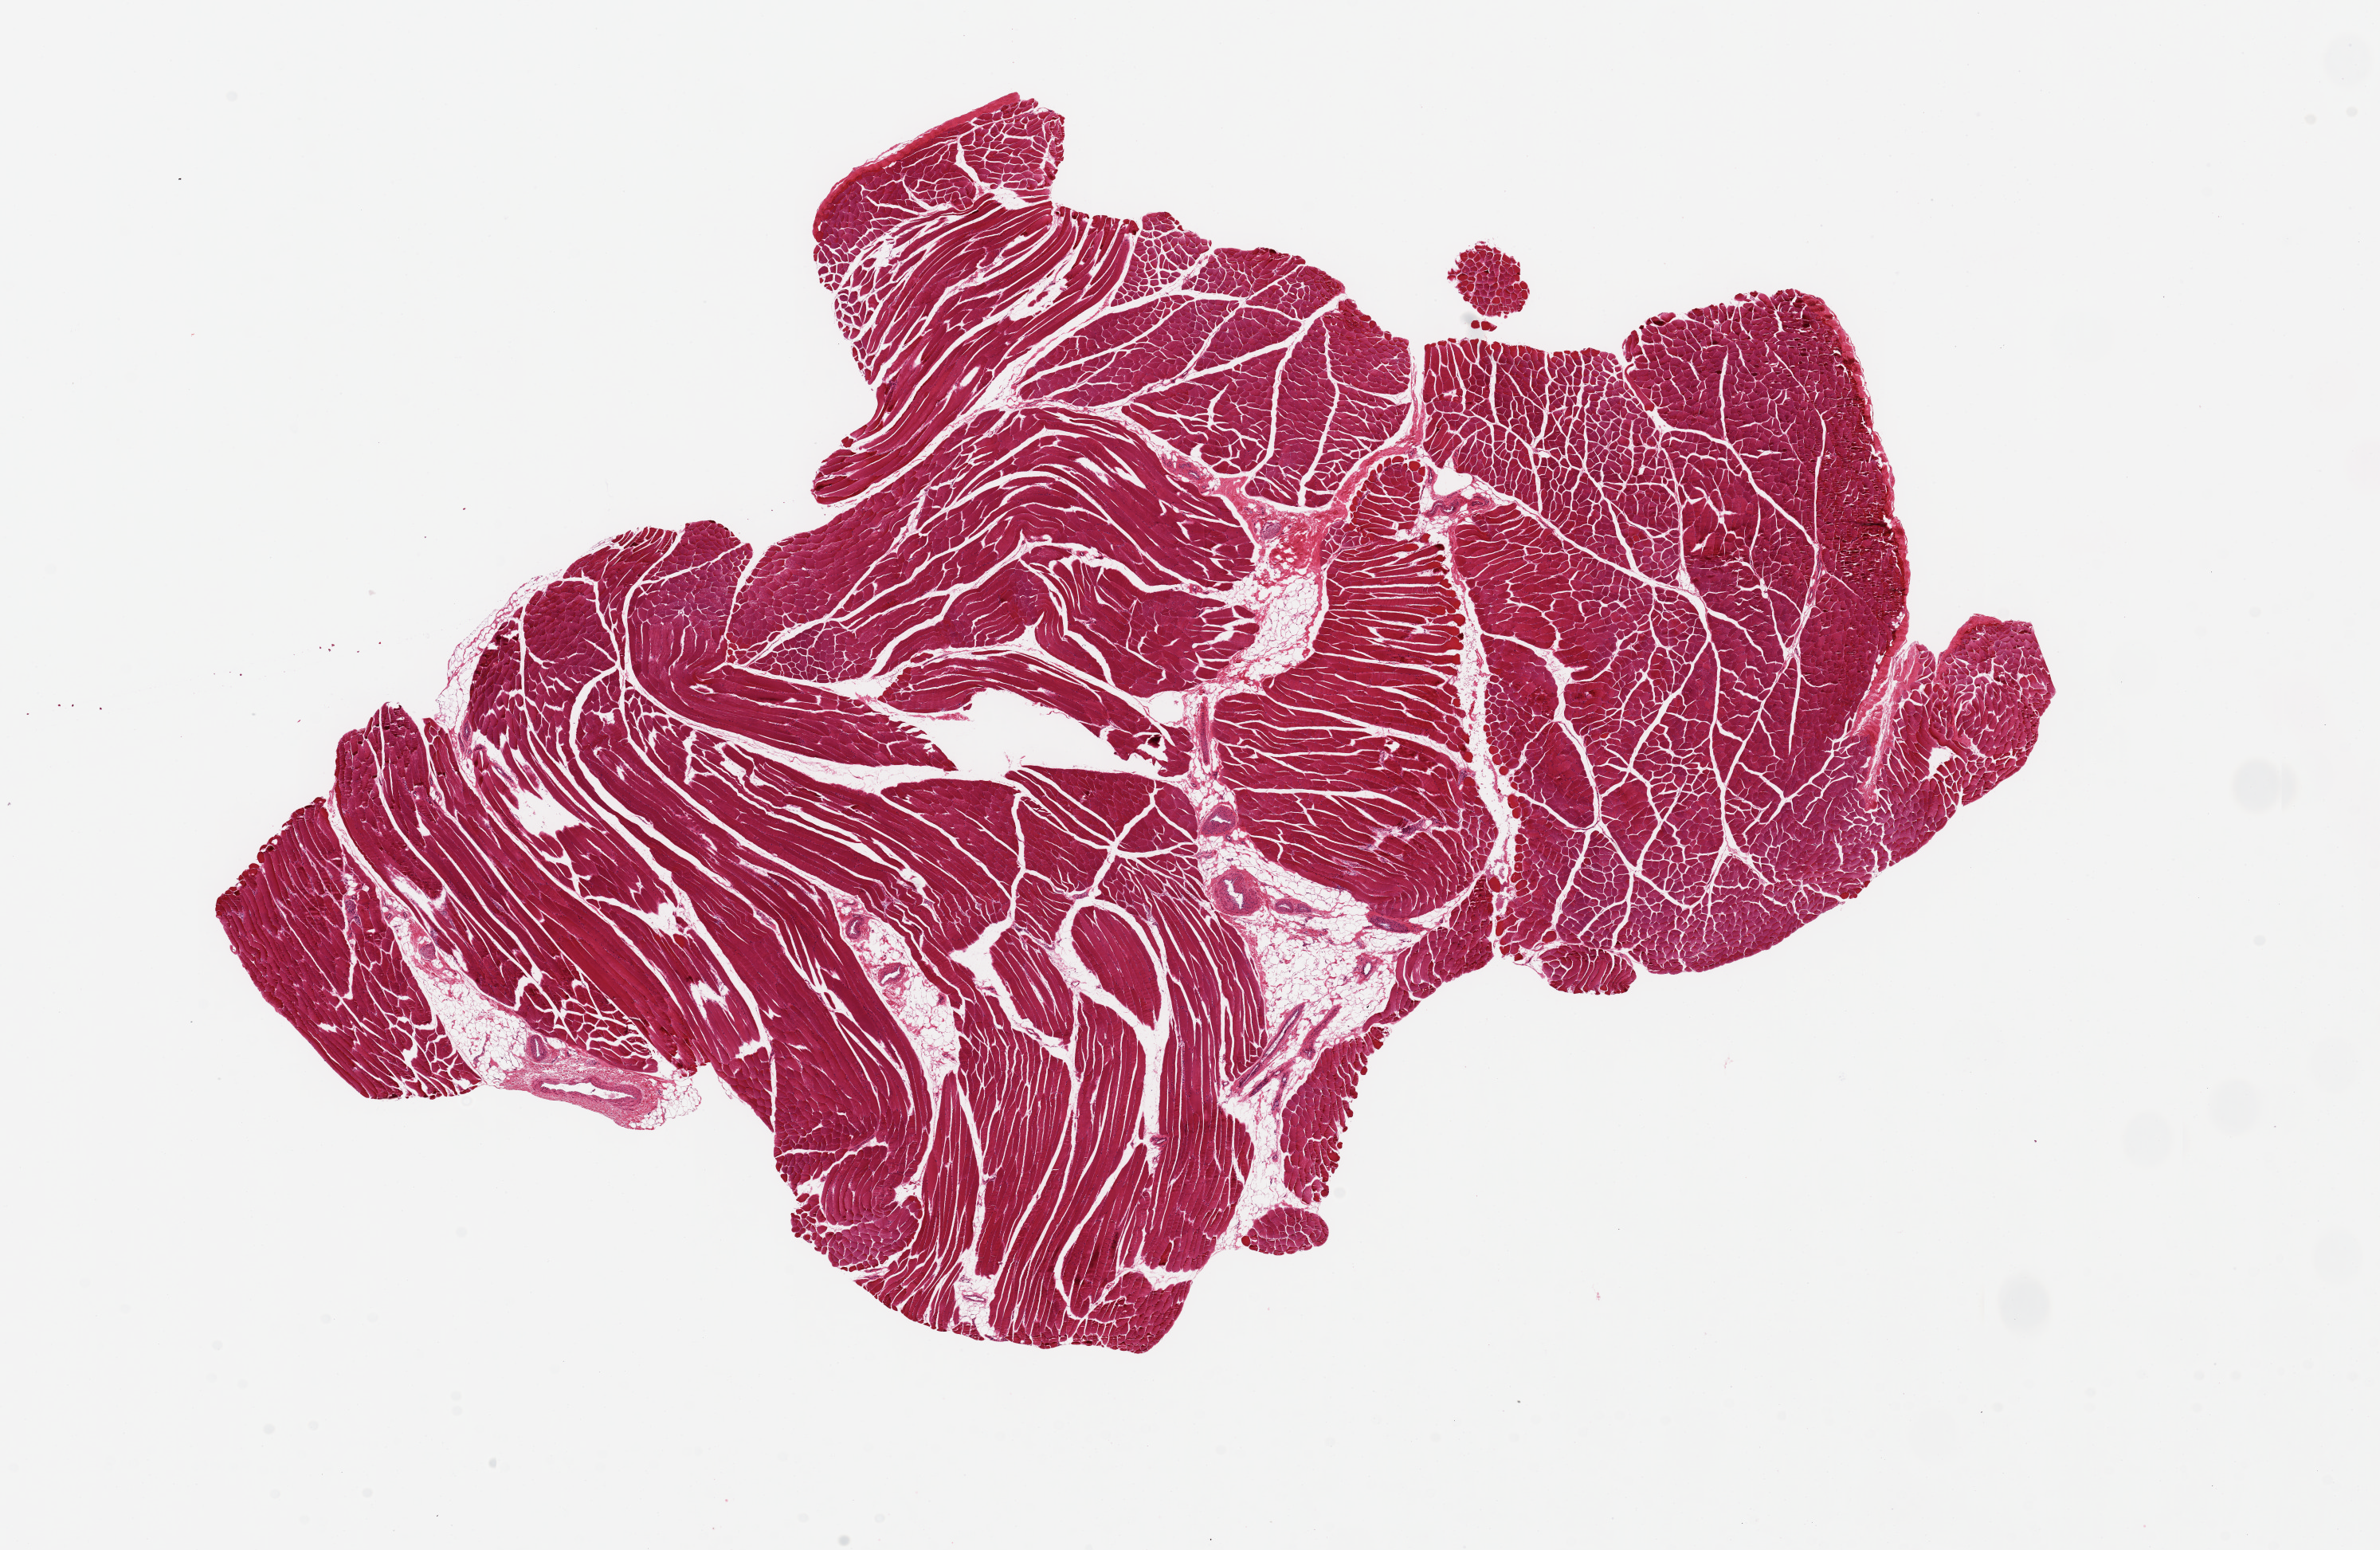
Whole-slide image, H&E stain, brightfield — low-resolution overview of the scanned area, about 23.6 x 15.4 mm (from a 20x scan), PAXgene-fixed paraffin-embedded (PFPE) section, sampled site (target tissue): skeletal muscle, tissue donor sample. Donor sex: male.
* review note (as recorded): 1piece ~17x12mm. Minimal interstitial fat